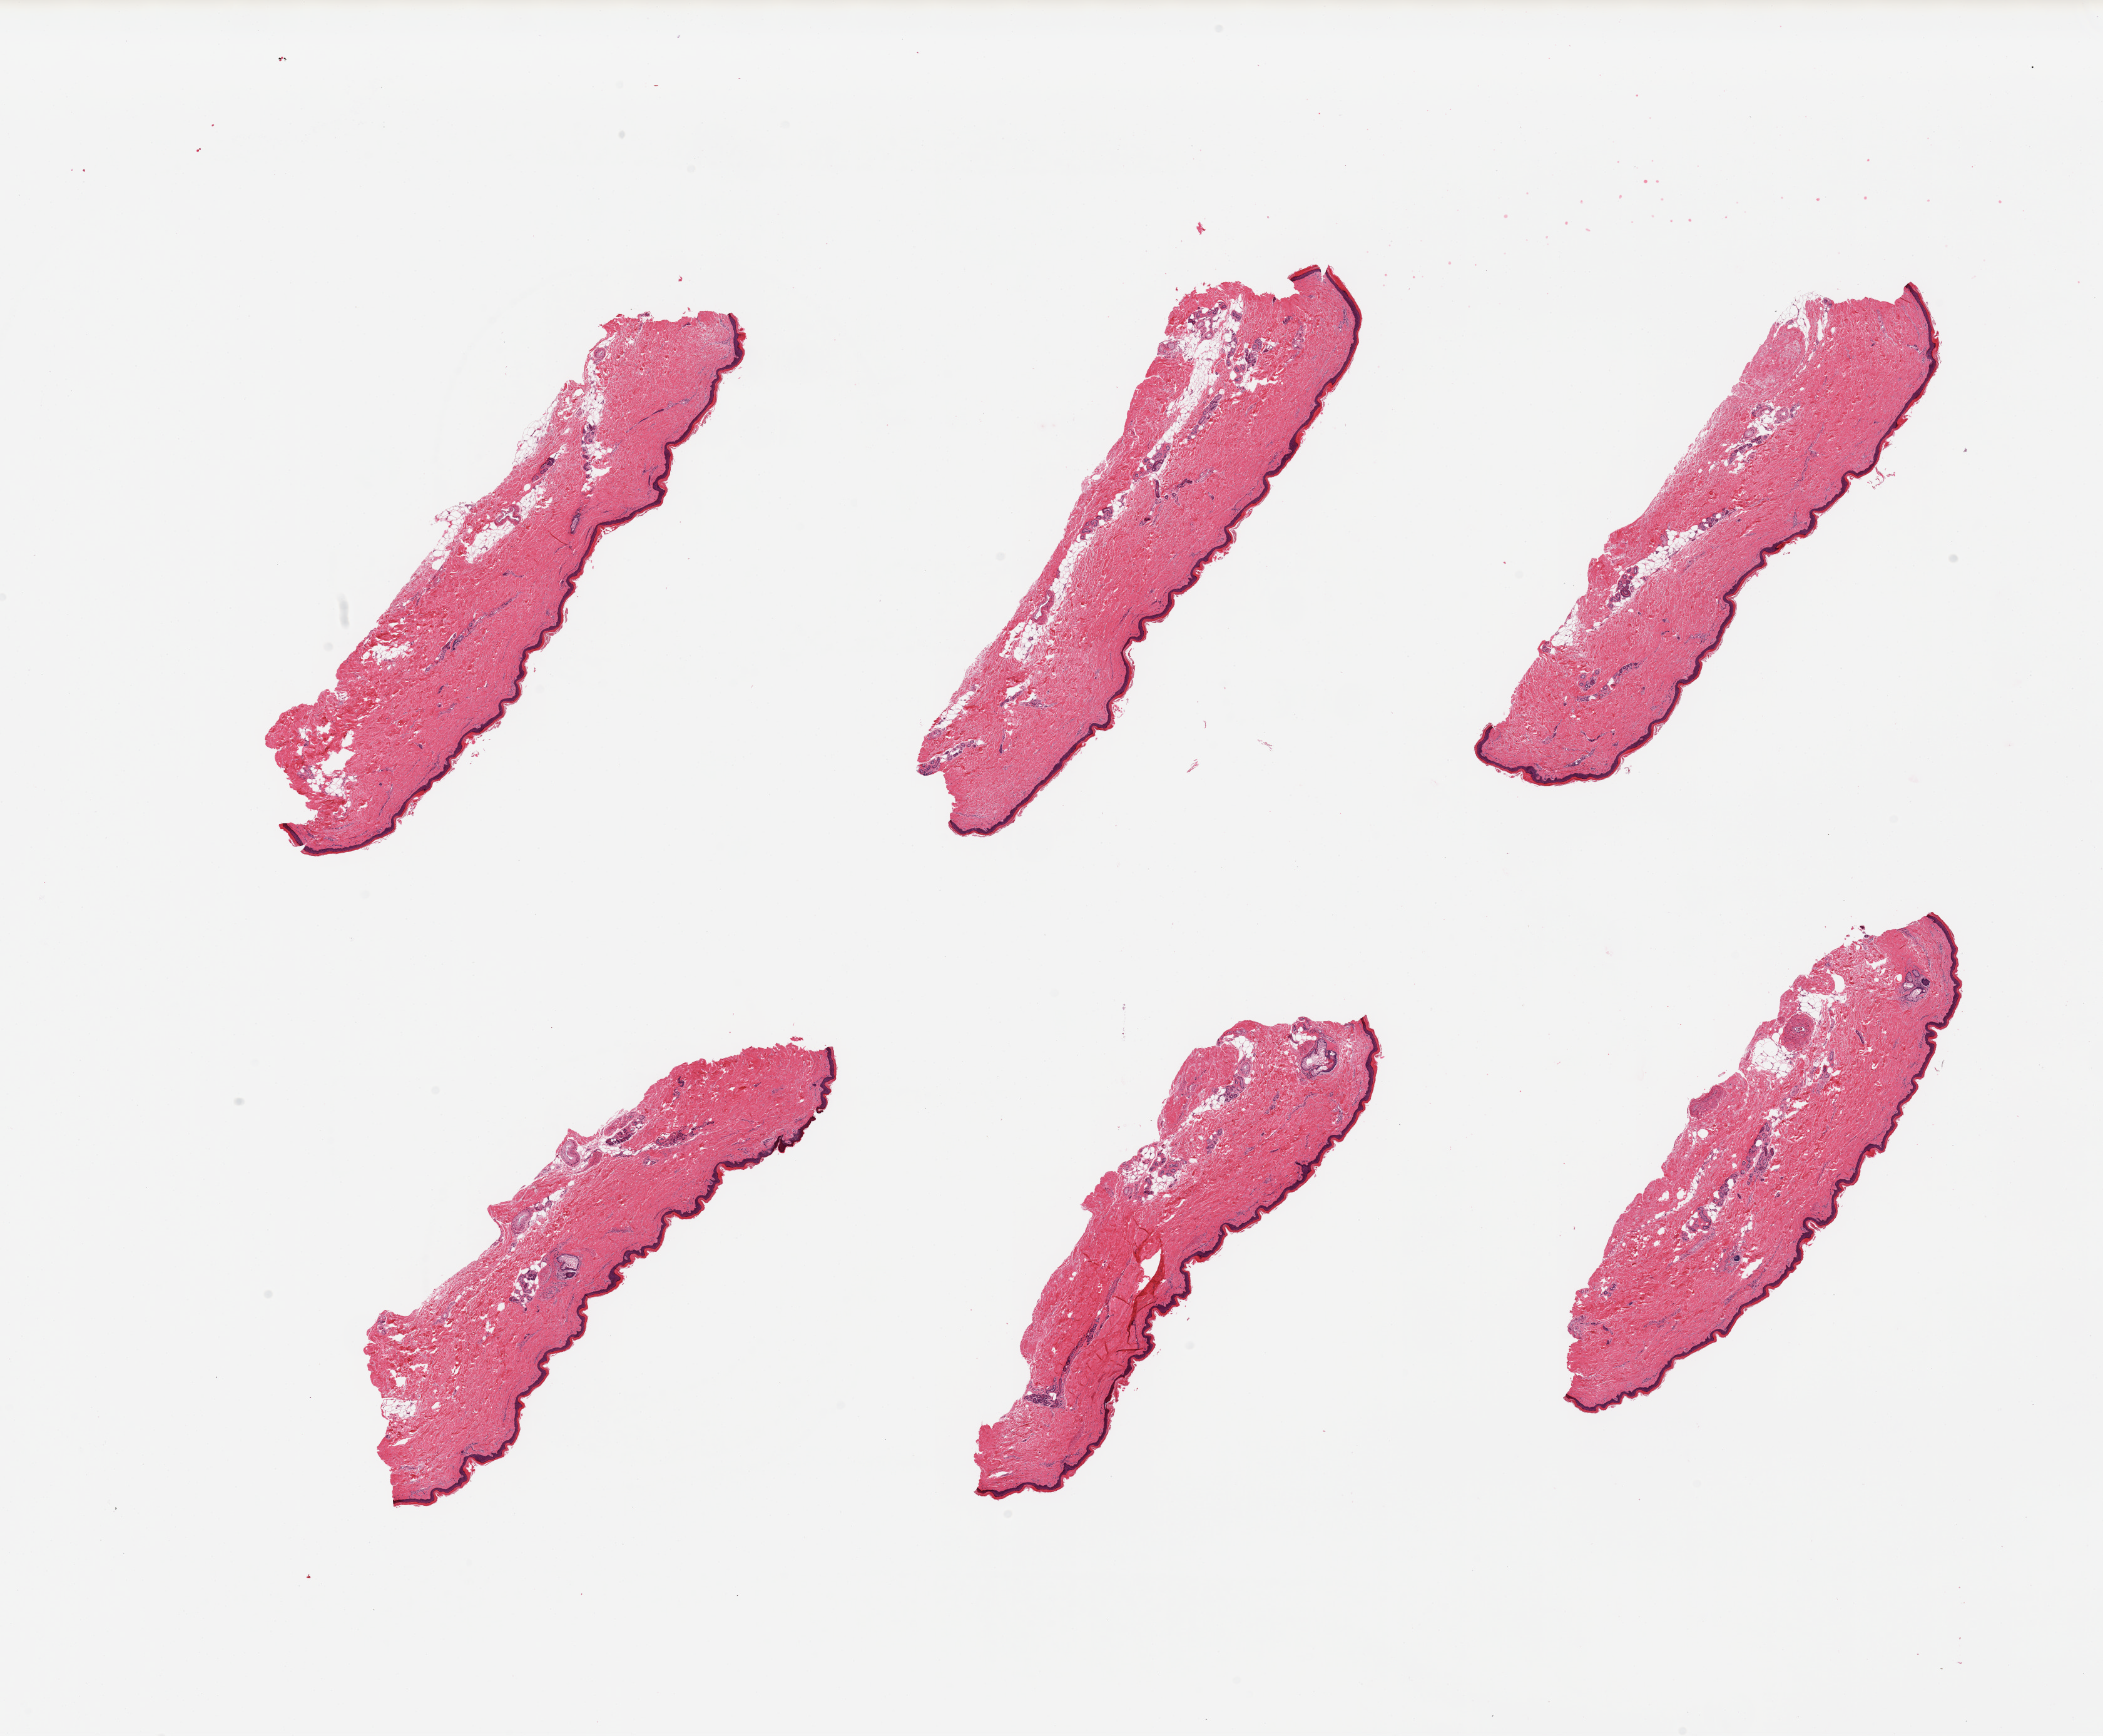
Digitized hematoxylin and eosin (H&E)-stained section — whole scanned area (about 26.6 x 21.9 mm) shown as a low-resolution overview; PAXgene-fixed paraffin-embedded (PFPE) section; section of skin of lower leg (target tissue); tissue donor sample. Donor: male.
Pathologist's review note for this sample: 6 pieces, no dermal fat; squamous epithelium is ~40 microns.